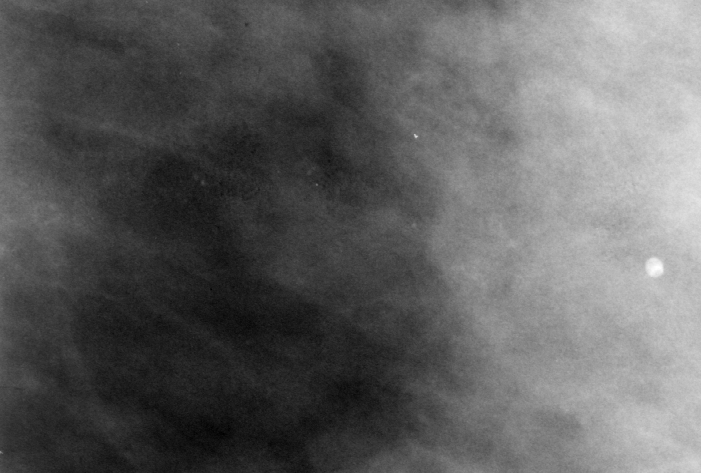
Region of interest cut from a scanned film mammogram (one marked finding); left breast; CC view.
Finding: calcifications, morphology amorphous, distribution segmental; BI-RADS assessment category 4; subtlety rating 2 on a 1 (subtle) to 5 (obvious) scale; pathology (as recorded): benign.